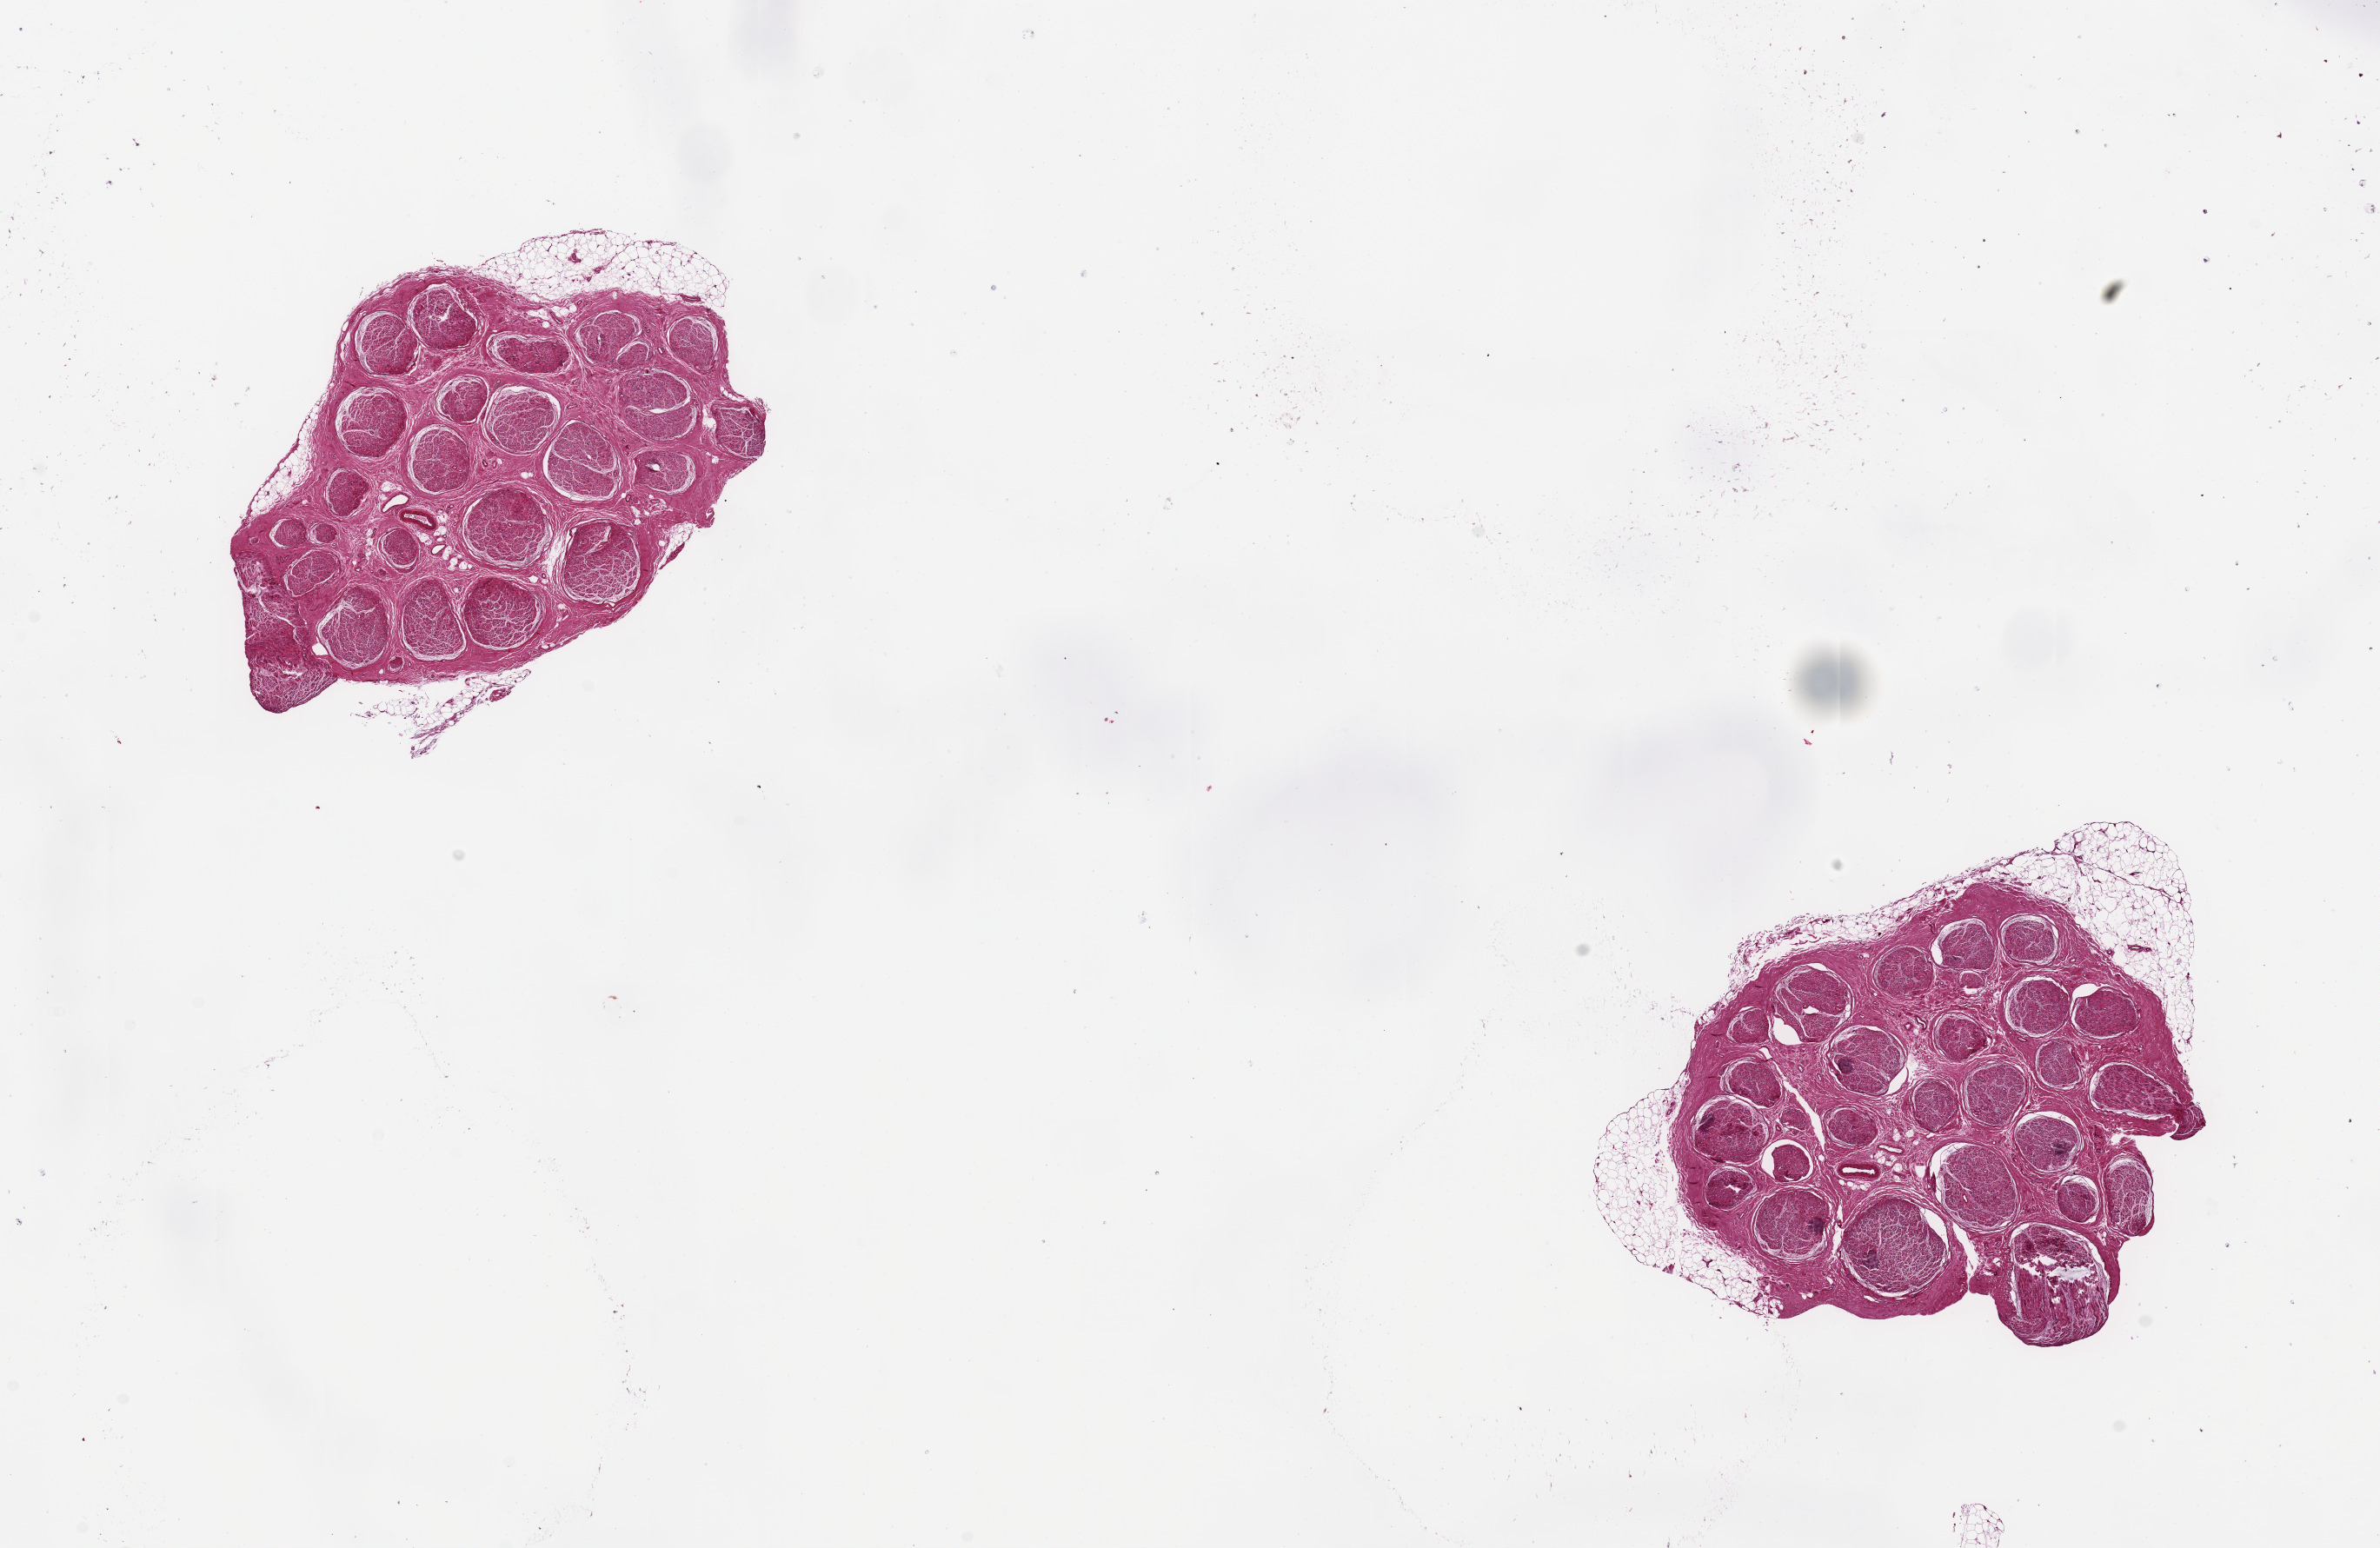
H&E whole-slide image — shown as a low-resolution overview of the whole scanned area (about 21.7 x 14.1 mm, acquisition: 20x scan). PAXgene-fixed, paraffin-embedded tissue. Sampled site (target tissue): tibial nerve. Donor tissue sample. Male donor.
• review note (as recorded): 2 ~5mm pieces, nearly clean, 0.5-1mm tags of adipose tissue